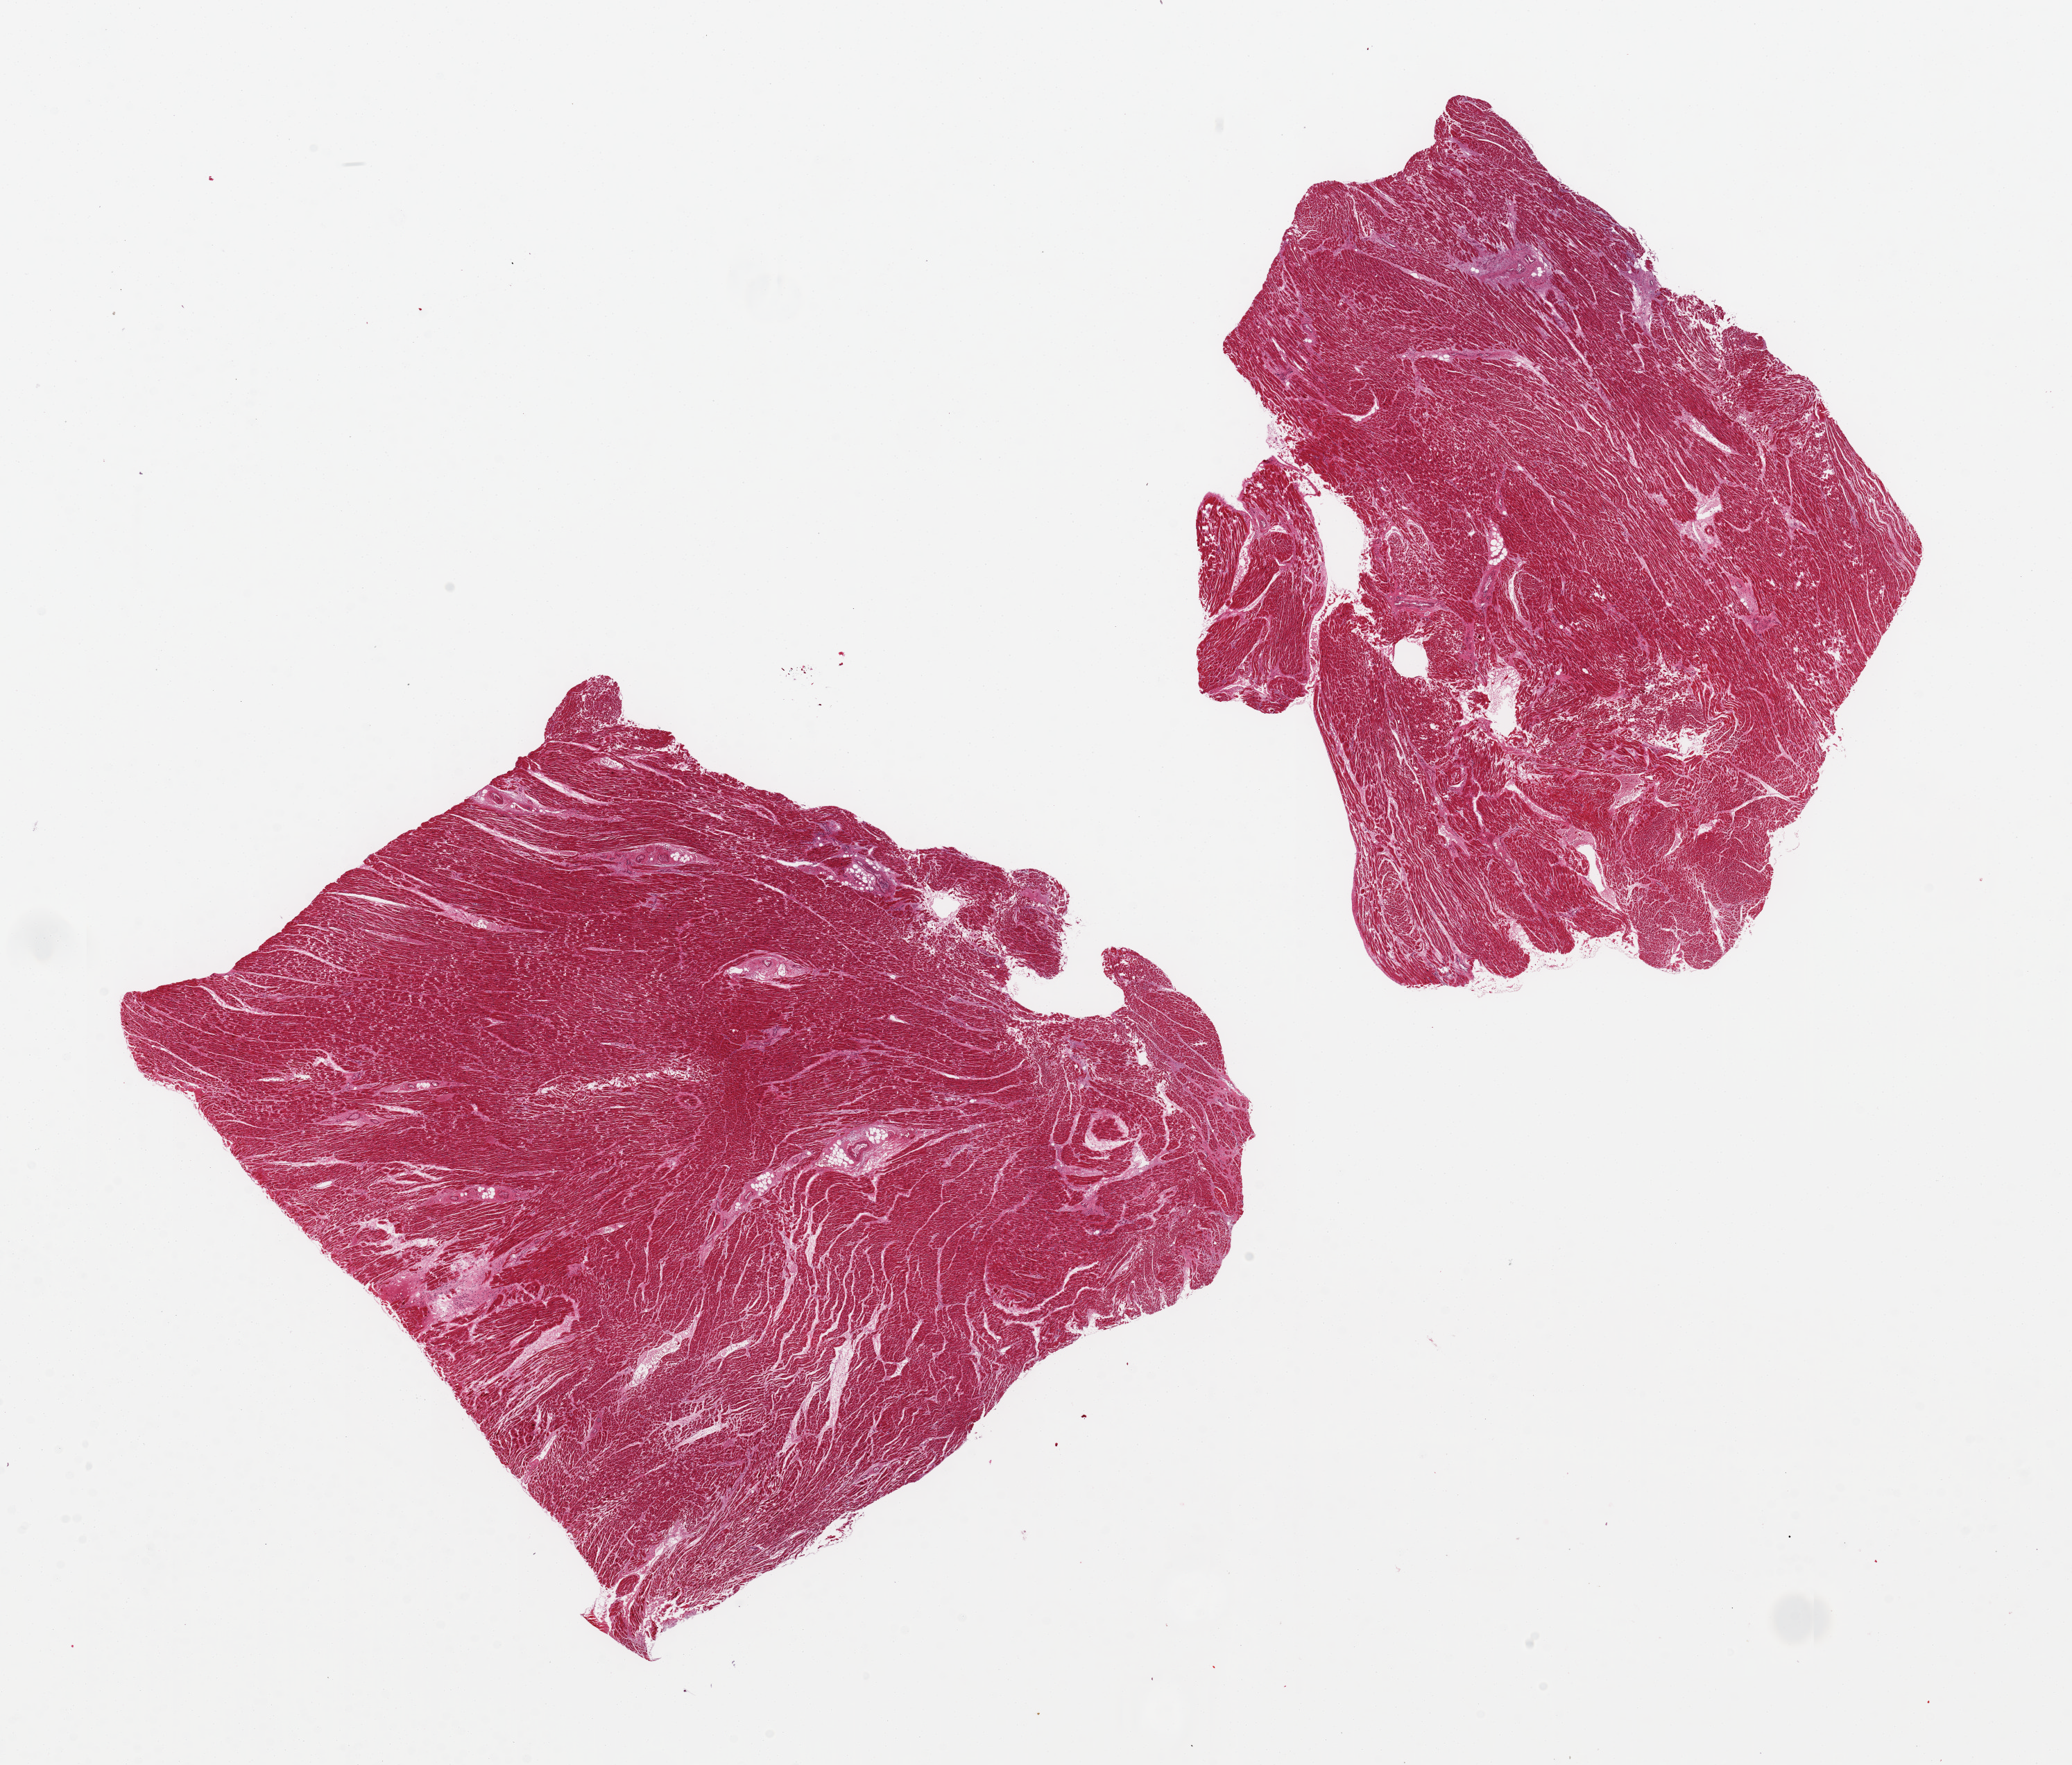
H&E whole-slide image — whole scanned area (about 23.6 x 20.1 mm) shown as a low-resolution overview; PAXgene-fixed paraffin-embedded (PFPE) section; section of heart (target tissue); donor tissue sample.
Reviewer comment on this tissue sample: 2 pieces, 9x9 & 9x8 mm; hypertrophic fibers; patchy early ischemia (hypereosinophilia).